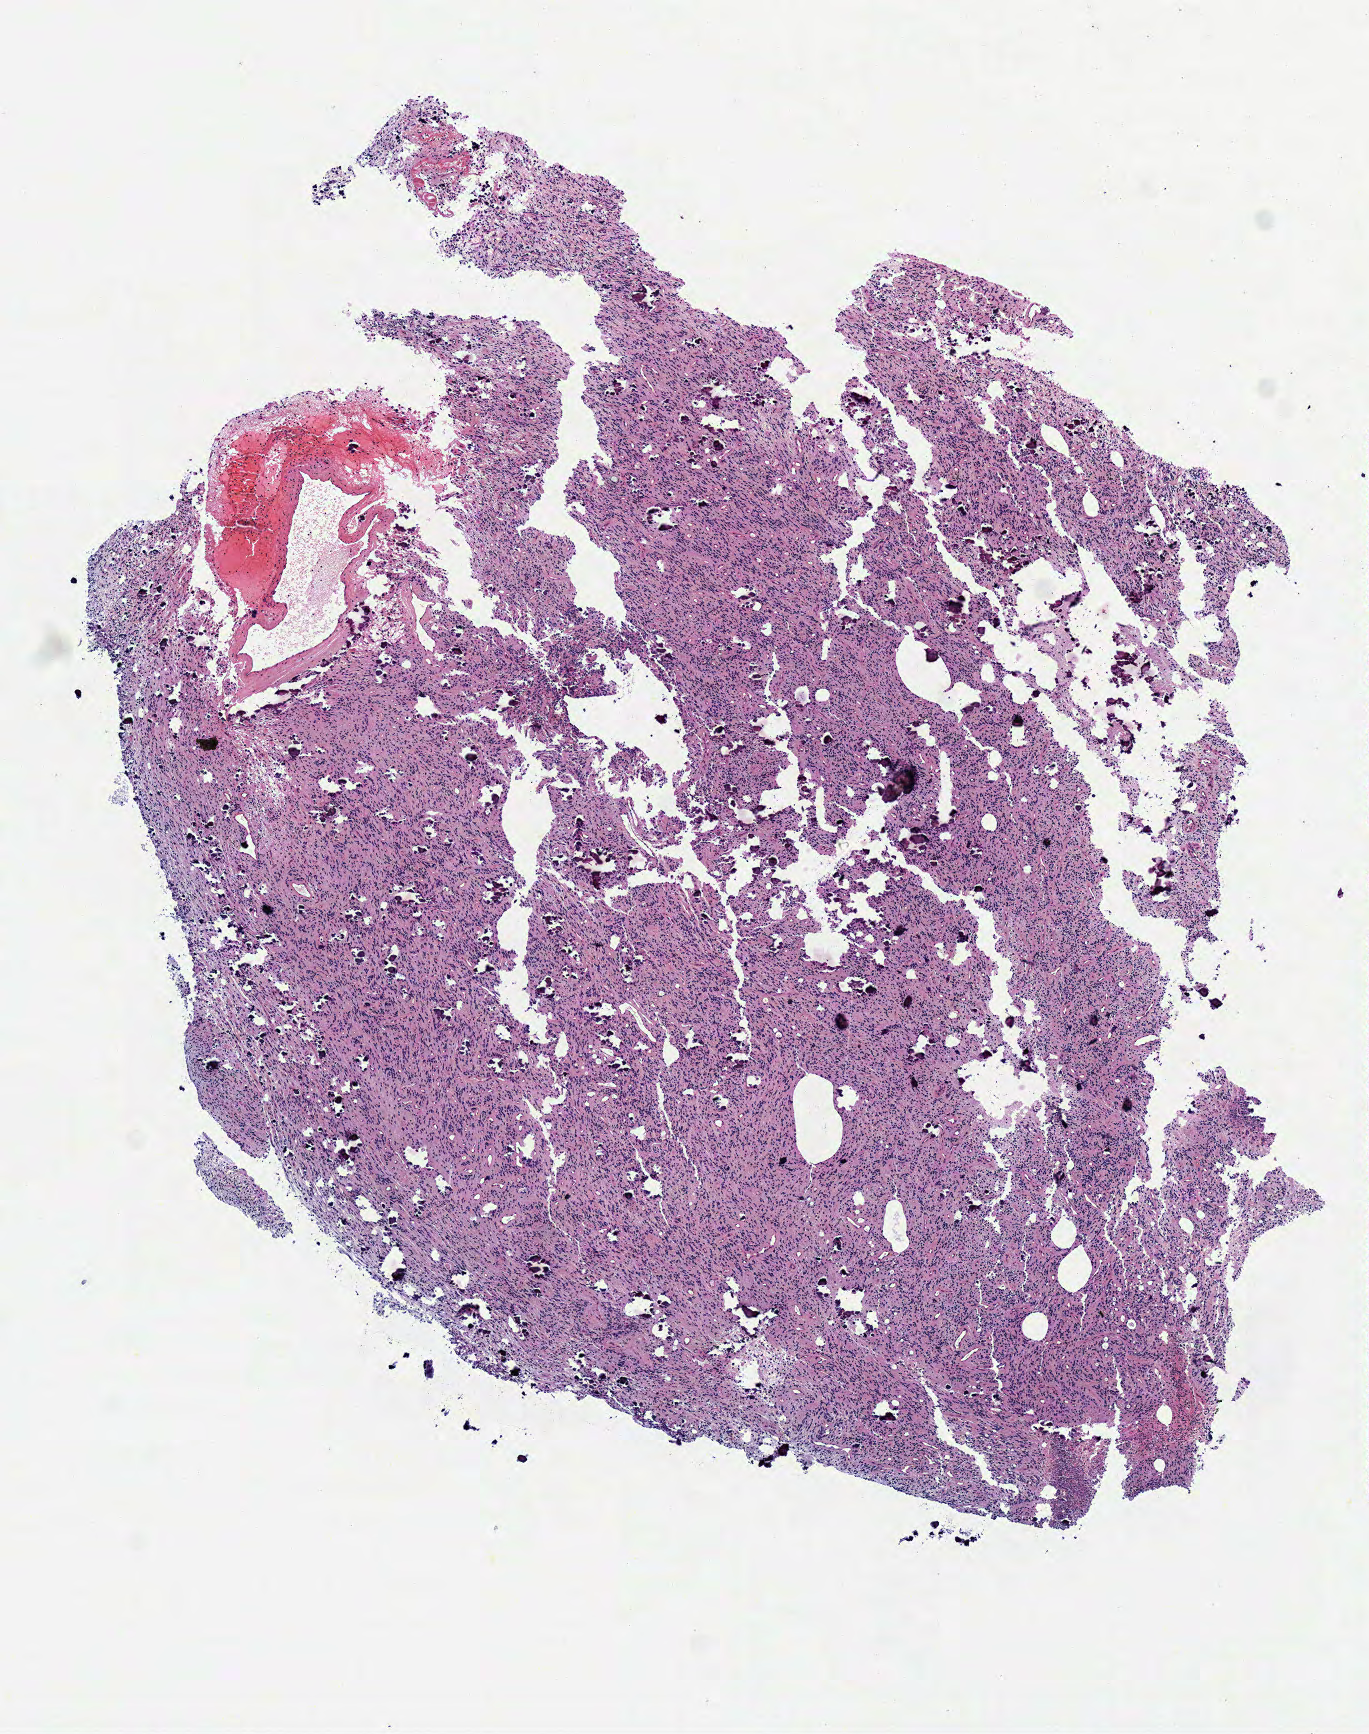
Hematoxylin and eosin (H&E) stained whole-slide image — a low-resolution overview of the entire scanned area, about 5.4 x 6.8 mm, frozen section, sample: primary tumour, brain. Patient: female, age at initial diagnosis 24 years. Pathologist review of this section (percent, as recorded): tumour cells 100%, tumour nuclei 80%.
Histologic diagnosis: Oligodendroglioma, anaplastic (cerebrum).